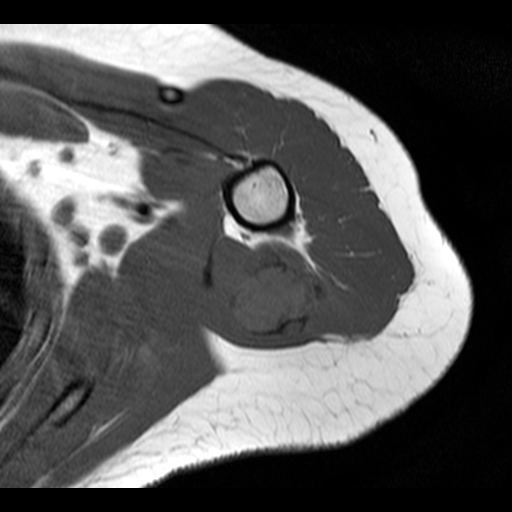
MRI of an extremity soft-tissue mass, one axial slice. Slice 6 of 20 in the series (ordered by position). 4 mm slice thickness. 512 × 512 image matrix, field of view 150 × 150 mm. Female patient. From the clinical record (not read from this slice): histological type: malignant fibrous histiocytoma; grade: low; site of the primary tumour: left arm.
Outlined on this slice (manually delineated by an expert):
- gross tumour volume (mass): bounding box [x1, y1, x2, y2] px = [229, 240, 335, 340]